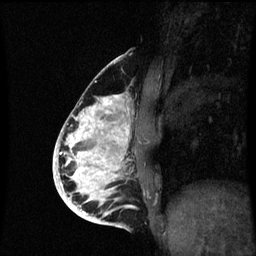
Breast MRI (dynamic contrast-enhanced), one sagittal slice; position 29 of 60 along the scan axis; dynamic contrast-enhanced series, image 2 of 3 at this slice position (ordered by acquisition); 1.5 T; TE 4.2 ms, TR 8.9 ms; 256 × 256 image matrix, field of view 200 × 200 mm. Patient: female, 35 years. Case-level facts recorded for this patient, not image findings: setting: breast cancer imaged before/during neoadjuvant chemotherapy; receptor status: HR-positive, HER2-negative.
Outlined on this slice (semi-automatically segmented with operator editing):
- analysis volume of interest (the breast-tissue region the enhancement analysis was run in; not a lesion): bounding box <66,94,143,215> (left, top, right, bottom; pixels)
- tumour enhancement mask (voxels above the 70 % enhancement threshold inside the analysis volume of interest): <66,94,130,215>